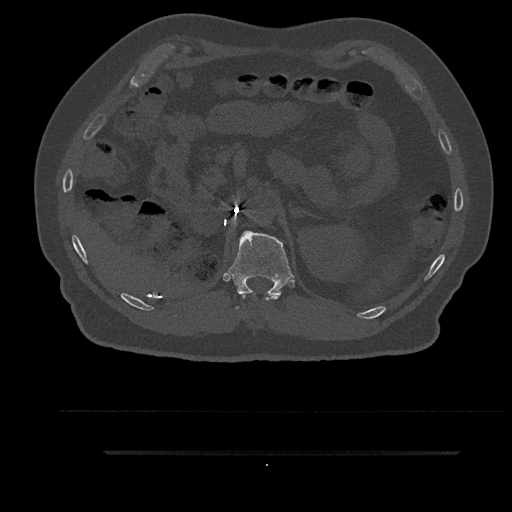
CT including the spine, one axial slice. Position 260 of 797 along the scan axis. Reconstruction kernel Br40s/3. 120 kVp. Bone window (W 1800 / L 400 HU). 0.5 mm slice thickness. 512 × 512 image matrix. Male patient, age 63 years. From the clinical record (not read from this slice): primary cancer: renal; vertebrae with lytic lesions (as recorded): T8.
Annotated regions visible in this slice (semi-automatically segmented with operator editing):
- T11 vertebra: bounding box (x1, y1, x2, y2) in pixels: (242, 294, 279, 301)
- T12 vertebra: (226, 230, 294, 309)